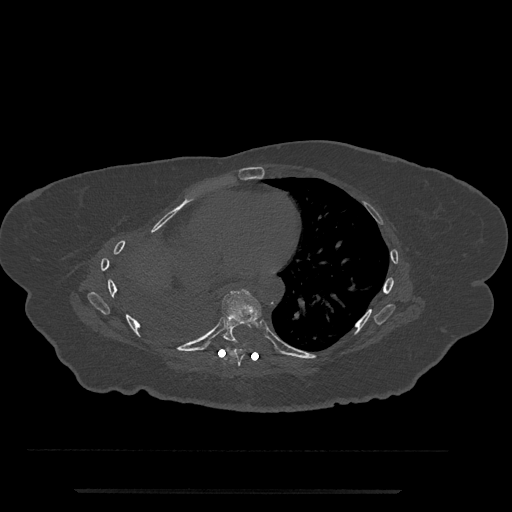
CT including the spine, one axial slice; slice 415 of 797 in the series (ordered by position); reconstruction kernel Br40s/3; 120 kVp; bone window (W 1800 / L 400 HU); 512 × 512 image matrix. Female patient, age 51 years. From the clinical record (not read from this slice): primary cancer: neuro; vertebrae with lytic lesions (as recorded): T8.
Outlined on this slice (semi-automatic segmentation, software-assisted and operator-edited):
- T7 vertebra: box from (x=224, y=347) to (x=245, y=366) px
- T8 vertebra: (x=222, y=289)–(x=262, y=341)